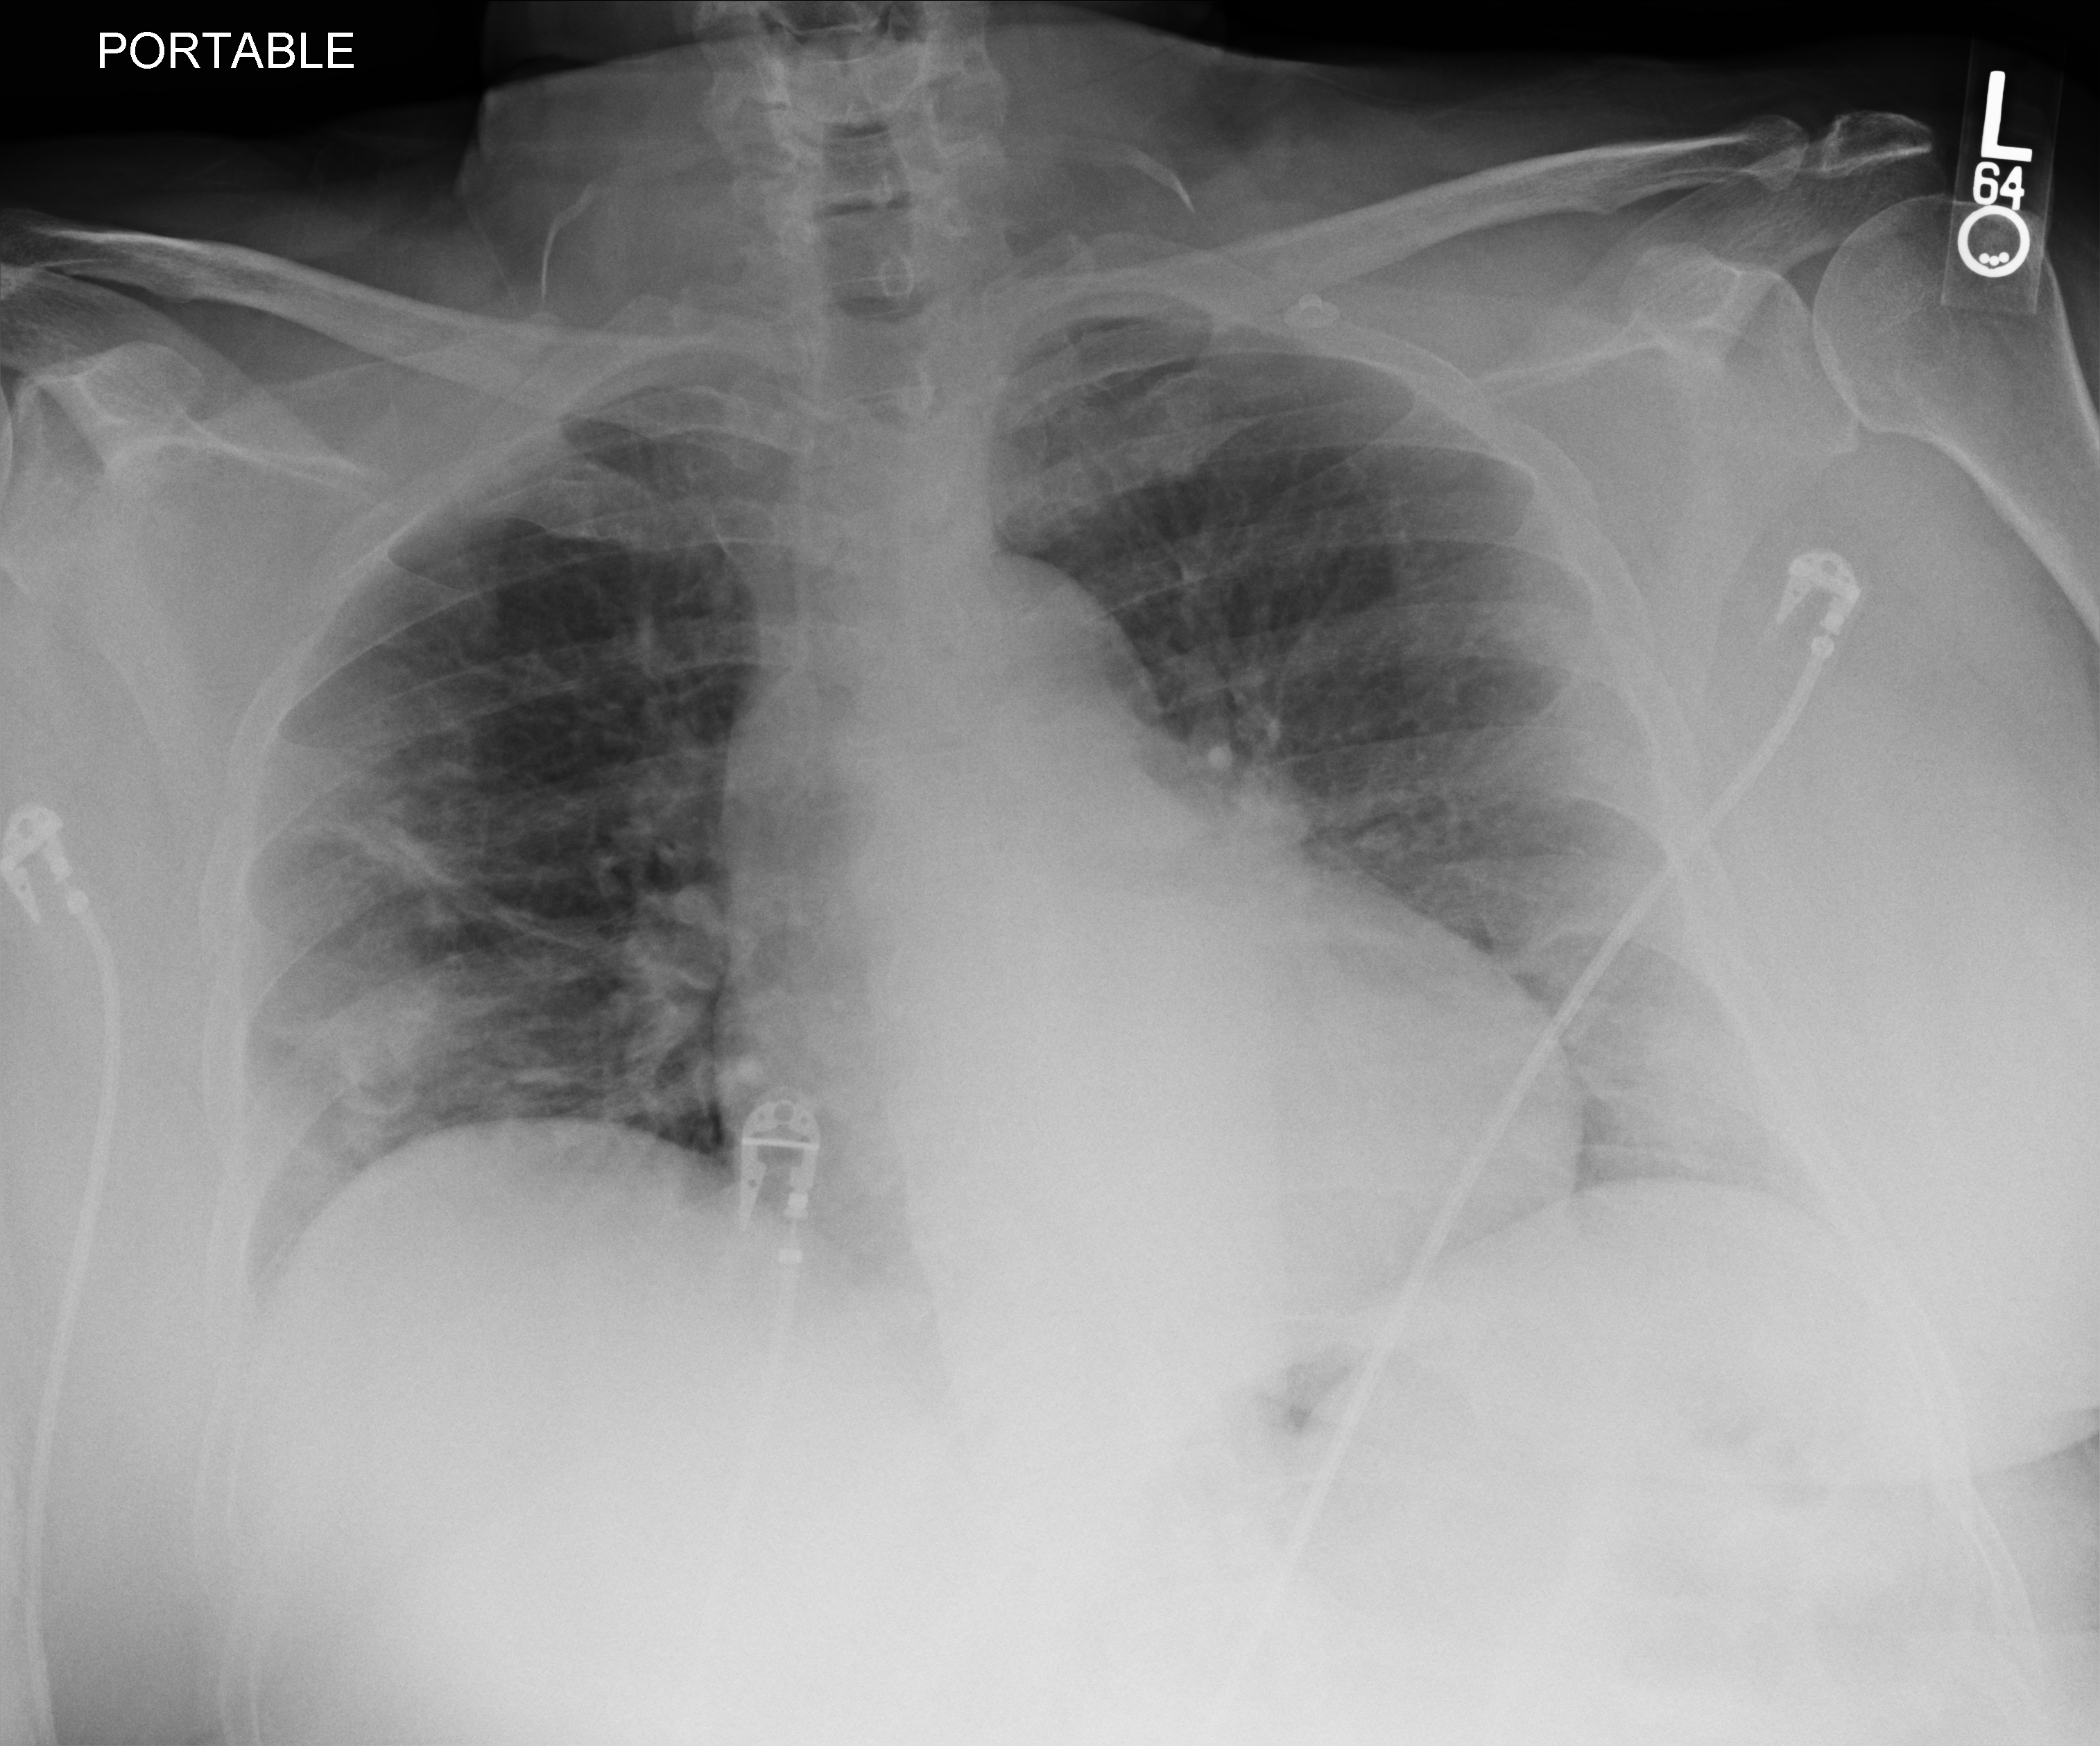
Portable chest radiograph, anteroposterior (AP) projection. Patient hospitalised with COVID-19; female, aged 60–74 years.
Admission-level facts for this patient (not findings on this image; timing relative to this image not recorded): mechanically ventilated during this hospital stay: no; admitted to intensive care during this hospital stay: no.